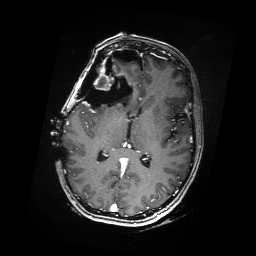
Brain MRI from a brain-tumour surgery series, one axial slice. Position 89 of 176 along the scan axis. T1-weighted post-contrast. 256 × 256 image matrix, field of view 256 × 256 mm. From the clinical record (not read from this slice): histopathology: Metastatic Carcinoma from Breast primary; tumour location: Right Frontal.
Outlined on this slice (manually delineated by an expert):
- residual tumour: bounding box (x1, y1, x2, y2) in pixels: (88, 68, 117, 89)